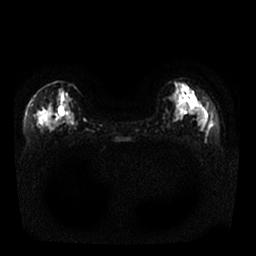
Breast MRI, one axial slice. Slice 10 of 25 in the series (ordered by position). Diffusion-weighted series; image 2 of 4 stored at this slice position (different b-values; order by instance number). 1.5 T. 4 mm slice thickness. 256 × 256 image matrix. Female patient.
Outlined on this slice (expert manual segmentation):
- tumour on diffusion-weighted imaging: box from (x=37, y=115) to (x=50, y=129) px